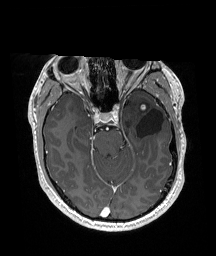
Brain MRI from a brain-tumour surgery series, one axial slice; position 114 of 192 along the scan axis; T1-weighted post-contrast; 1 mm slice thickness; 216 × 256 image matrix. Case-level facts recorded for this patient, not image findings: histopathology: Glioneuronal tumor; WHO grade: 2; tumour location: Left Superior Temporal Gyrus.
Annotated regions visible in this slice (outlined manually by an expert reader):
- previous resection cavity: bounding box (x1, y1, x2, y2) in pixels: (136, 109, 164, 138)
- tumour: (140, 104, 148, 112)